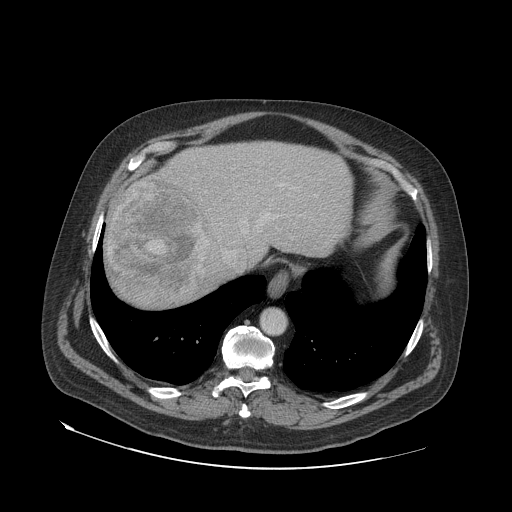
Contrast-enhanced abdominal CT (liver protocol), one axial slice; slice 61 of 79 in the series (ordered by position); reconstruction kernel STANDARD; soft-tissue window (W 400 / L 40 HU); 2.5 mm slice thickness; 512 × 512 image matrix. Case-level facts recorded for this patient, not image findings: diagnosis: hepatocellular carcinoma (patient treated with transarterial chemoembolisation; whether this scan precedes or follows treatment is not stated here); TNM stage (as recorded): Stage-IVA; Child-Pugh class: A.
Outlined on this slice (semi-automatically segmented with operator editing):
- abdominal aorta: box from (x=261, y=310) to (x=286, y=334) px
- liver parenchyma outside the tumour (the mass and vessels are separate outlines, so this box may not span the whole liver): (x=104, y=142)–(x=352, y=308)
- mass: (x=109, y=178)–(x=210, y=305)
- liver vessels: (x=225, y=184)–(x=283, y=254)